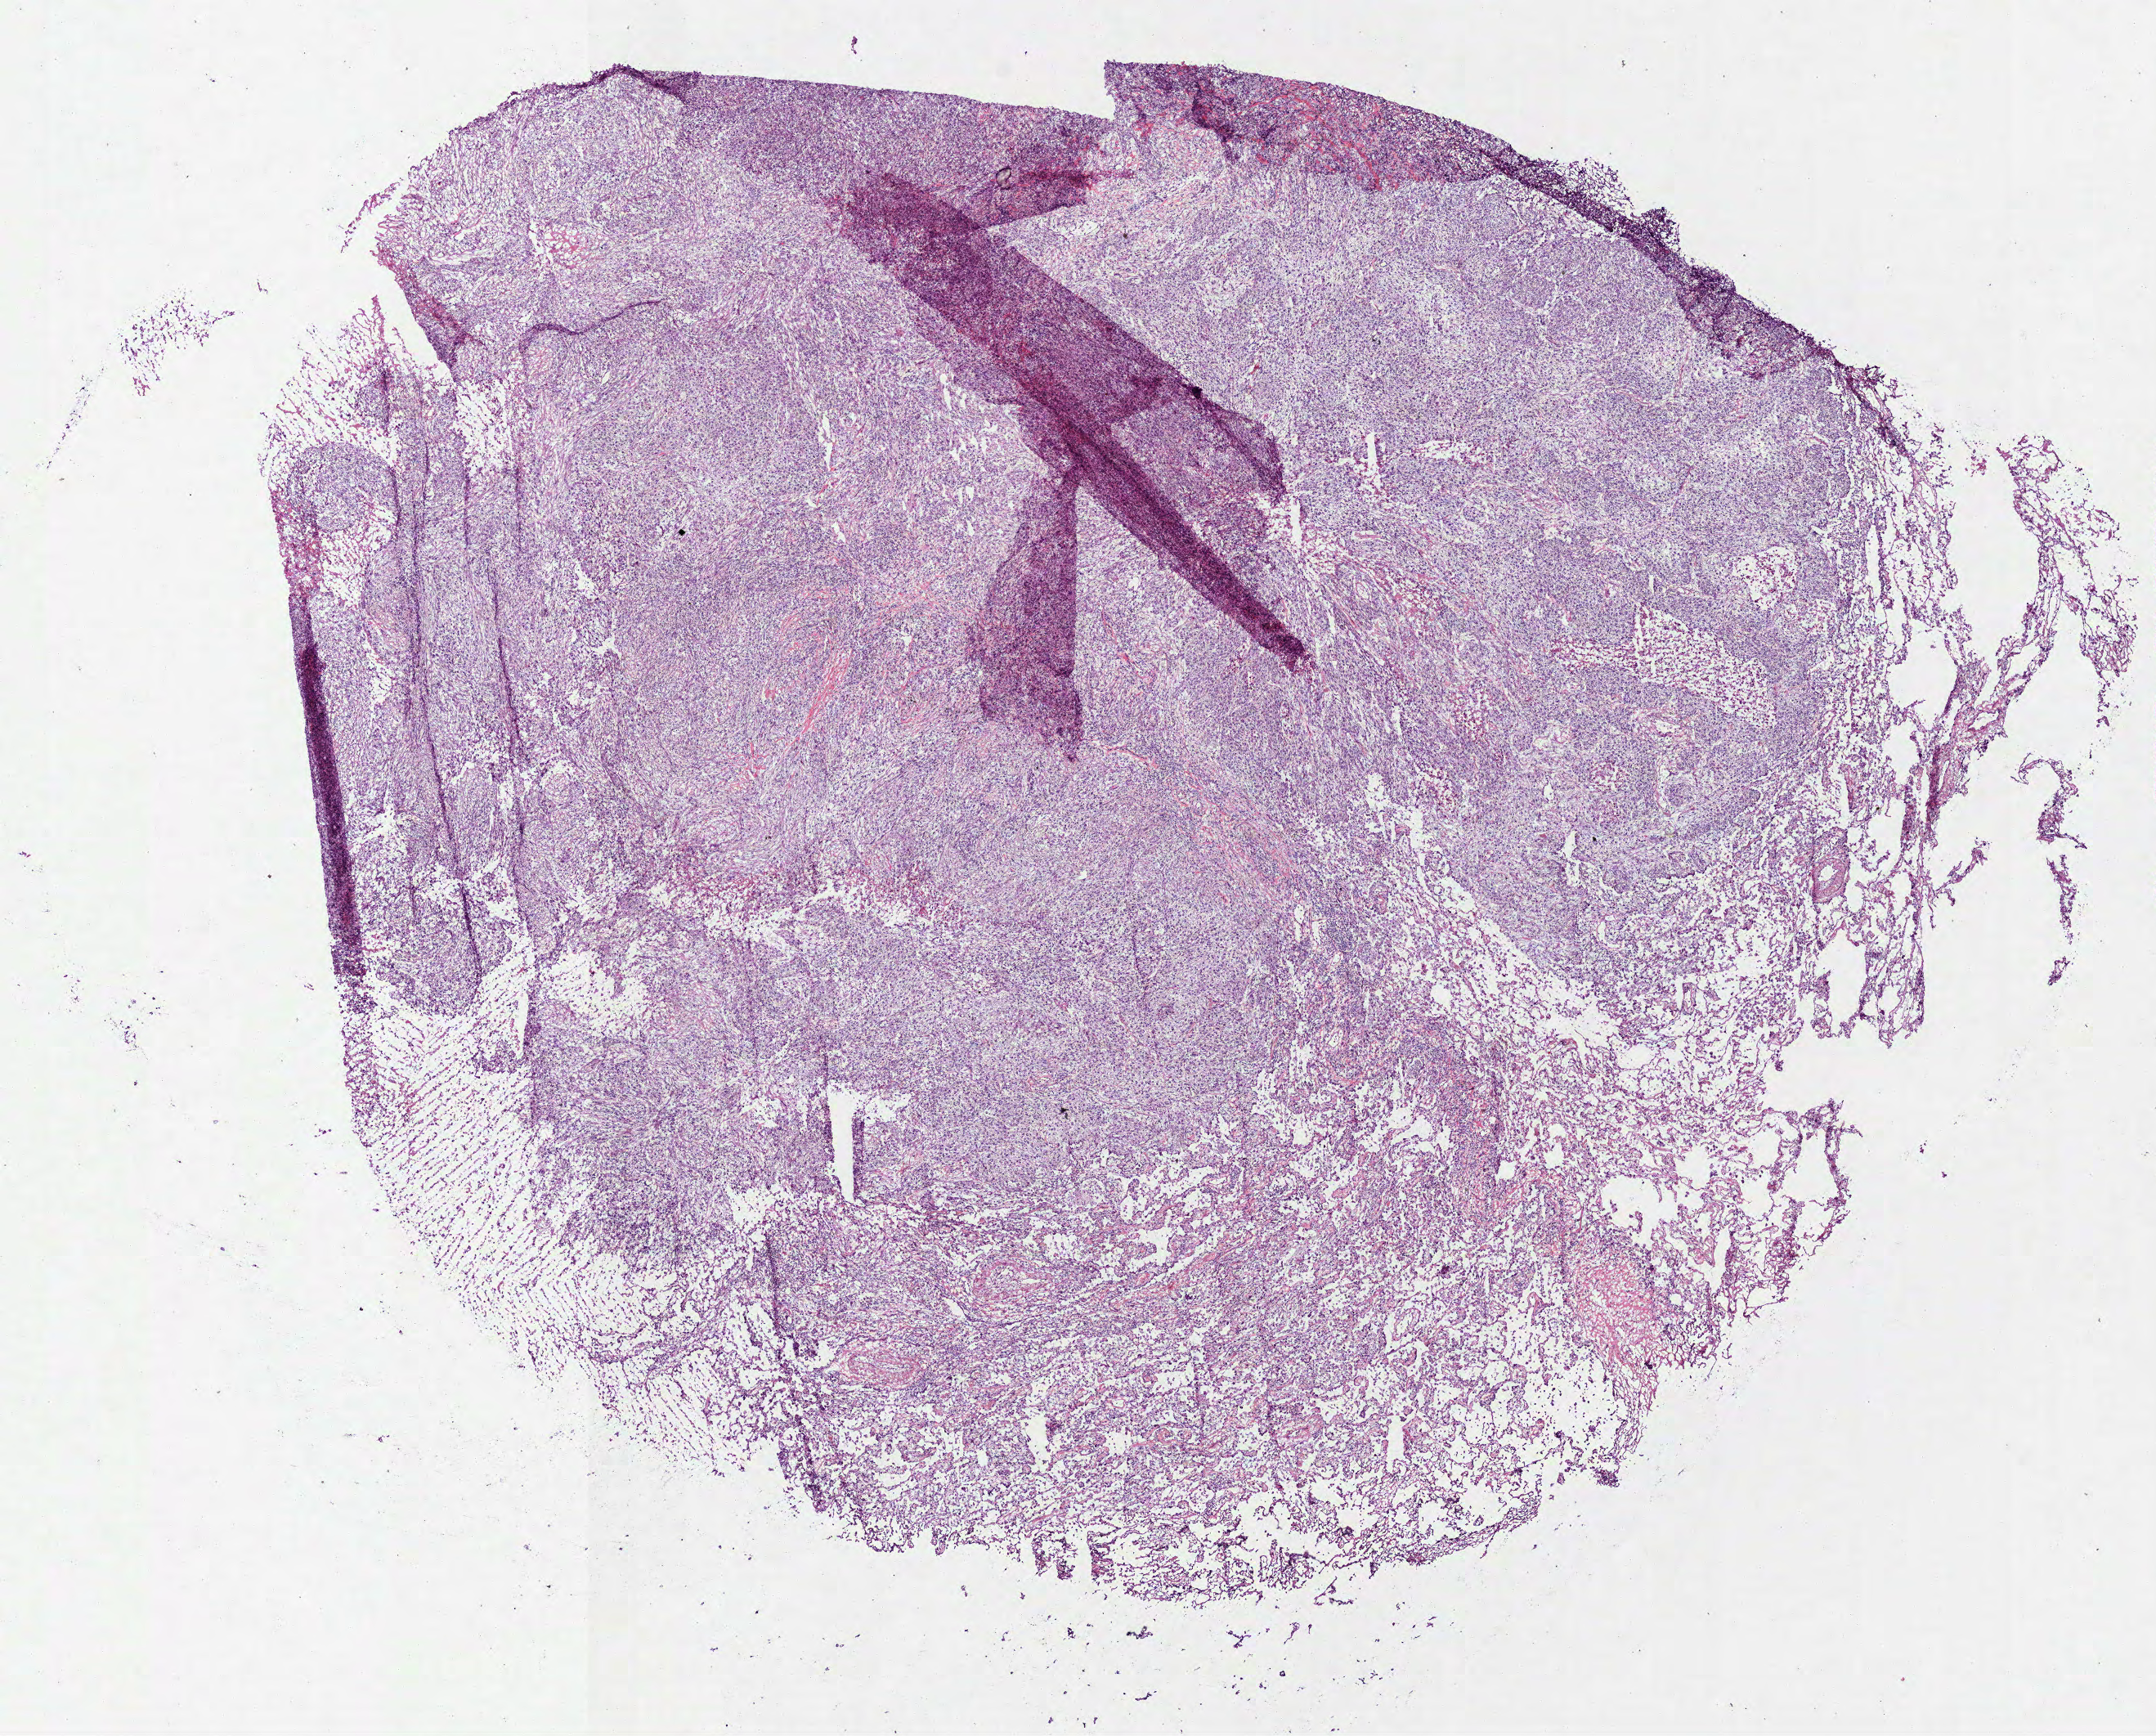
Whole-slide histology image, Hematoxylin and eosin (H&E) stained, a low-resolution overview of the entire scanned area, about 10.6 x 8.6 mm; frozen section from the bottom of the tissue portion; lung, primary tumour sample. Patient: female, age at initial diagnosis 77 years. Slide review estimates, as recorded: tumour cells 70%, tumour nuclei 70%, normal cells 15%, stromal cells 15%, necrosis 0%.
- diagnosis: Squamous cell carcinoma, NOS
- AJCC pathologic stage: IB (7th edition)